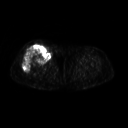
FDG PET of an extremity soft-tissue mass (from a PET/CT study), one axial slice. Position 248 of 311 along the scan axis. 3.27 mm slice thickness. 128 × 128 image matrix, field of view 500 × 500 mm. Female patient, age 57 years. Case-level facts recorded for this patient, not image findings: histological type: pleiomorphic undifferentiated sarcoma; grade: high; site of the primary tumour: right quadricep.
Annotated regions visible in this slice (expert contour drawn on MRI and transferred to this co-registered scan by the dataset authors):
- tumour plus oedema (research contour): bounding box <23,46,49,72> (left, top, right, bottom; pixels)
- tumour (research contour): <23,46,49,72>